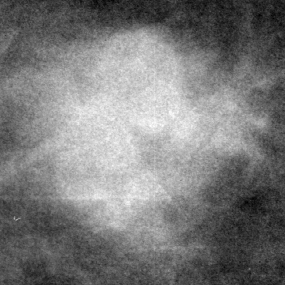
Region of interest cut from a scanned film mammogram (one marked finding), left breast, MLO view.
Mass, shape lobulated / irregular, margins ill defined; BI-RADS assessment category 4; subtlety rating 4 on a 1 (subtle) to 5 (obvious) scale; pathology (as recorded): malignant.